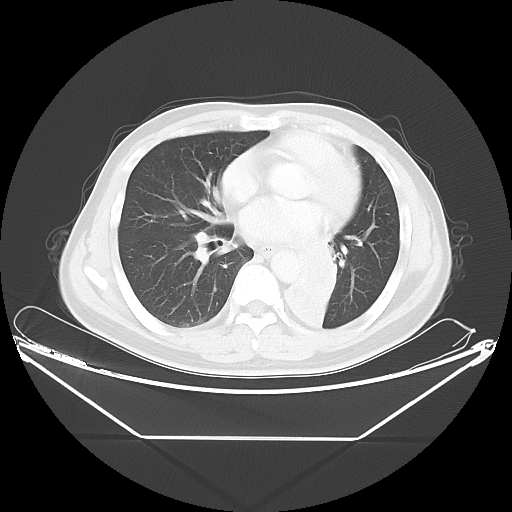
Chest CT, one axial slice; position 21 of 48 along the scan axis; reconstruction kernel LUNG; lung window (W 1500 / L -600 HU); 5 mm slice thickness; 512 × 512 image matrix, field of view 438 × 438 mm. Male patient, age 58 years. From the clinical record (not read from this slice): clinical TNM (as recorded): T3 N3 M0.
Structures marked on this image (bounding box drawn by a radiologist):
- lung tumour (recorded histology: squamous cell carcinoma): box from (x=267, y=198) to (x=354, y=348) px